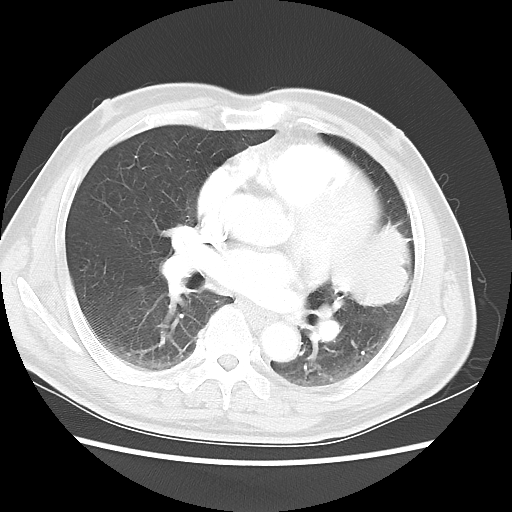
Chest CT, one axial slice. Position 24 of 50 along the scan axis. Lung window (W 1500 / L -600 HU). 5 mm slice thickness. 512 × 512 image matrix. Male patient, age 69 years. Case-level facts recorded for this patient, not image findings: clinical TNM (as recorded): T3 N1 M1a.
Annotated regions visible in this slice (rectangle marked by the reading radiologist):
- lung tumour (recorded histology: squamous cell carcinoma): bounding box <339,212,423,314> (left, top, right, bottom; pixels)